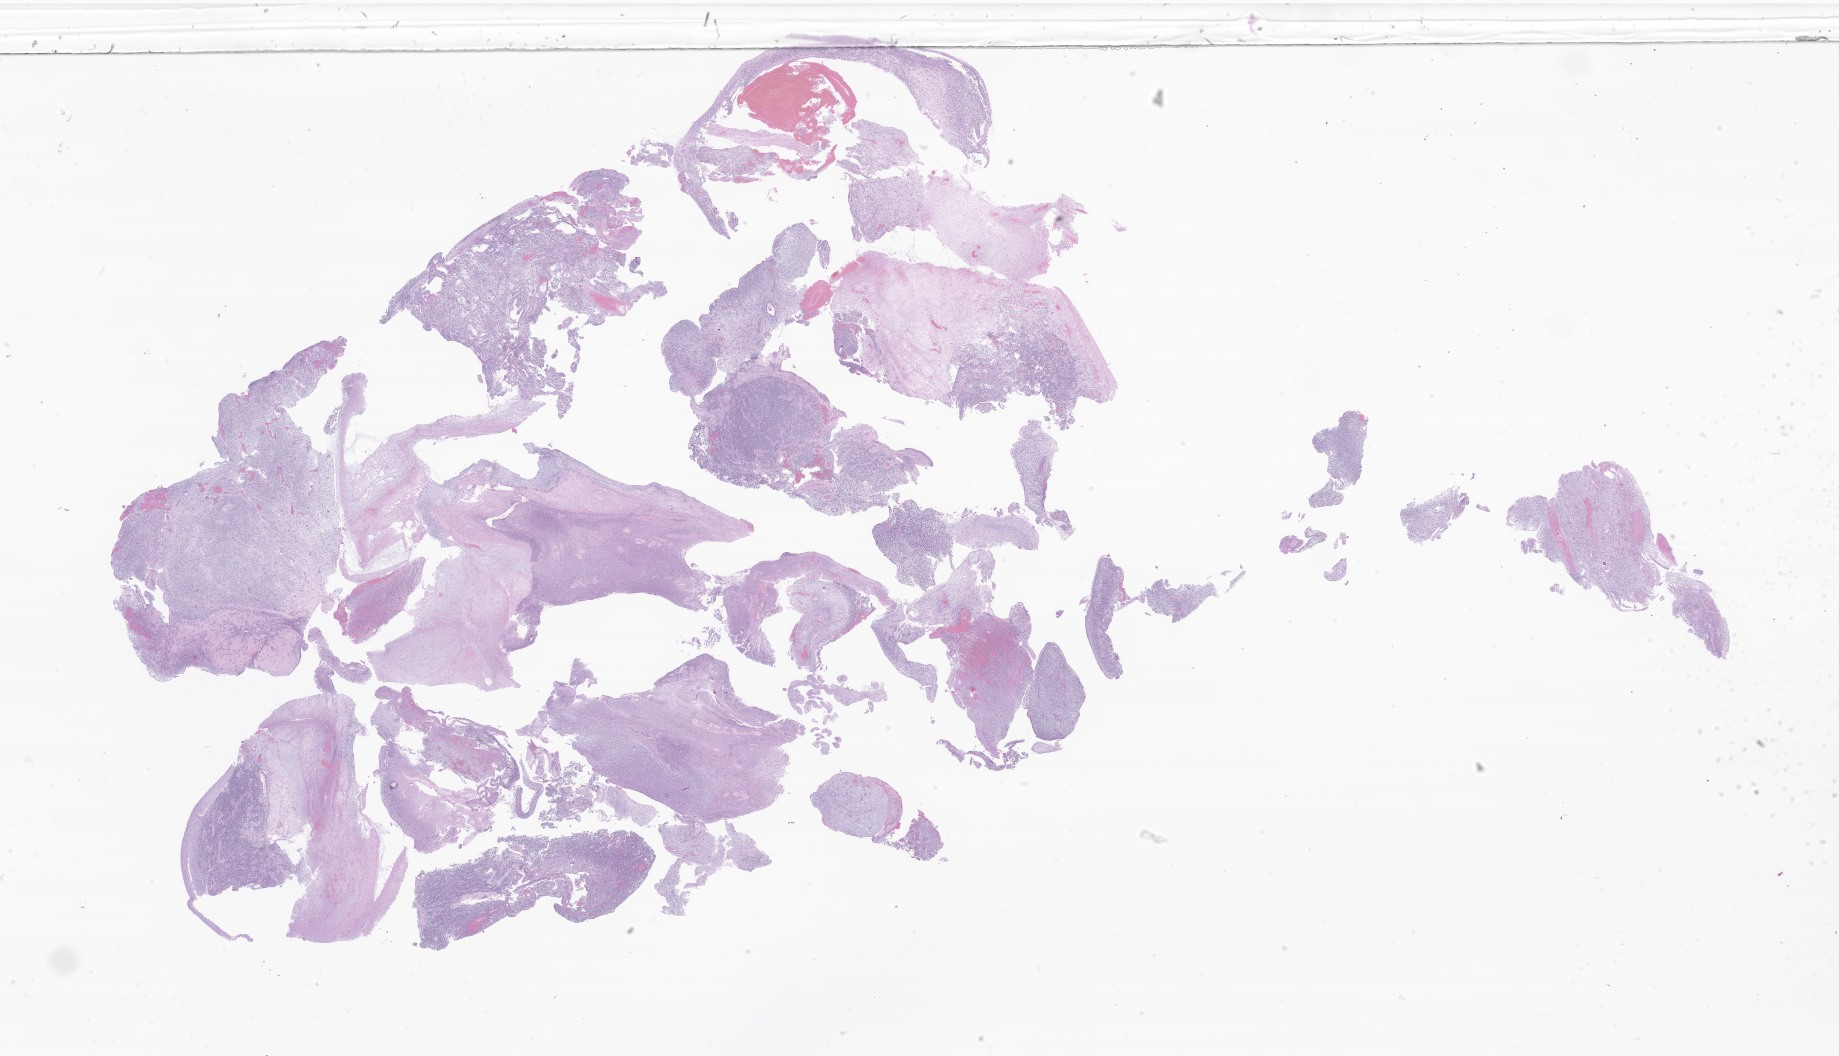
Whole-slide image, hematoxylin and eosin (H&E) stain of tumor tissue from the nasopharynx, whole scanned area (about 31.0 x 17.8 mm) shown as a low-resolution overview. Formalin-fixed paraffin-embedded section. Patient: female, age 51 months (4 years 3 months).
- diagnosis: Embryonal rhabdomyosarcoma, NOS